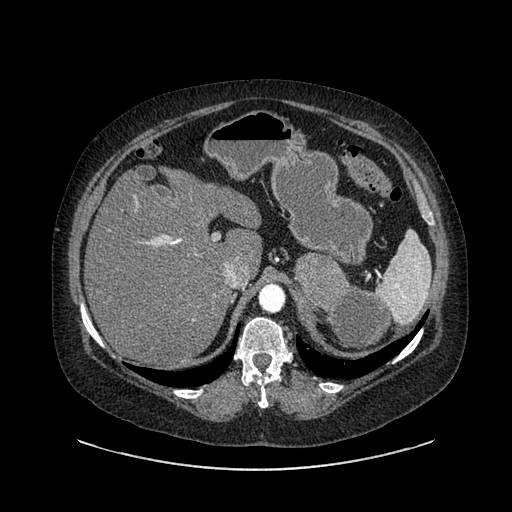
Contrast-enhanced abdominal CT, one axial slice. Position 615 of 769 along the scan axis. Reconstruction kernel SOFT. Soft-tissue window (W 400 / L 40 HU). 0.62 mm slice thickness. 512 × 512 image matrix, field of view 460 × 460 mm. Female patient, age 61 years. Case-level facts recorded for this patient, not image findings: diagnosis: adrenocortical carcinoma; tumour side: left adrenal; tumour size at pathology: 13 cm; Ki-67 index: 79 %; stage (as recorded): 2.
Annotated regions visible in this slice (semi-automatic segmentation, software-assisted and operator-edited):
- mass: bounding box (x1, y1, x2, y2) in pixels: (294, 253, 390, 351)